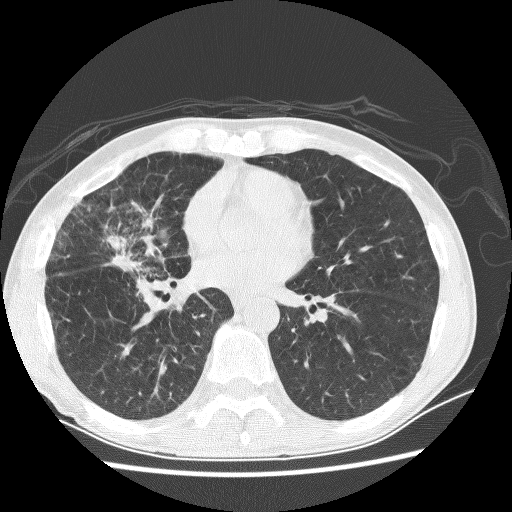
Low-dose screening chest CT, axial slice, first (baseline) screen, lung window (W 1500 / L -600 HU), 2.5 mm slice thickness, lung (sharp) reconstruction kernel (BONE), slice 141 of 256 in the series, 512 × 512 image matrix, field of view 340 × 340 mm. Male, age 67 years at enrolment. Current smoker at enrolment.
Expert reader's lesion annotation, bounding box [x1, y1, x2, y2] px = [83, 215, 175, 285]. Screening reader's record for this exam (one nodule recorded; not confirmed to be the boxed lesion): non-calcified nodule or mass ≥4 mm, right middle lobe, 28 × 18 mm, spiculated (stellate) margins, soft tissue attenuation. Official screen result: positive, change unspecified: nodule(s) >= 4 mm or enlarging nodule(s), mass(es), or other non-specific abnormalities suspicious for lung cancer. Later outcome: lung cancer diagnosed 69 days after this screen — adenocarcinoma, NOS, right middle lobe, stage IV (AJCC 6th edition), 60 mm at pathology.